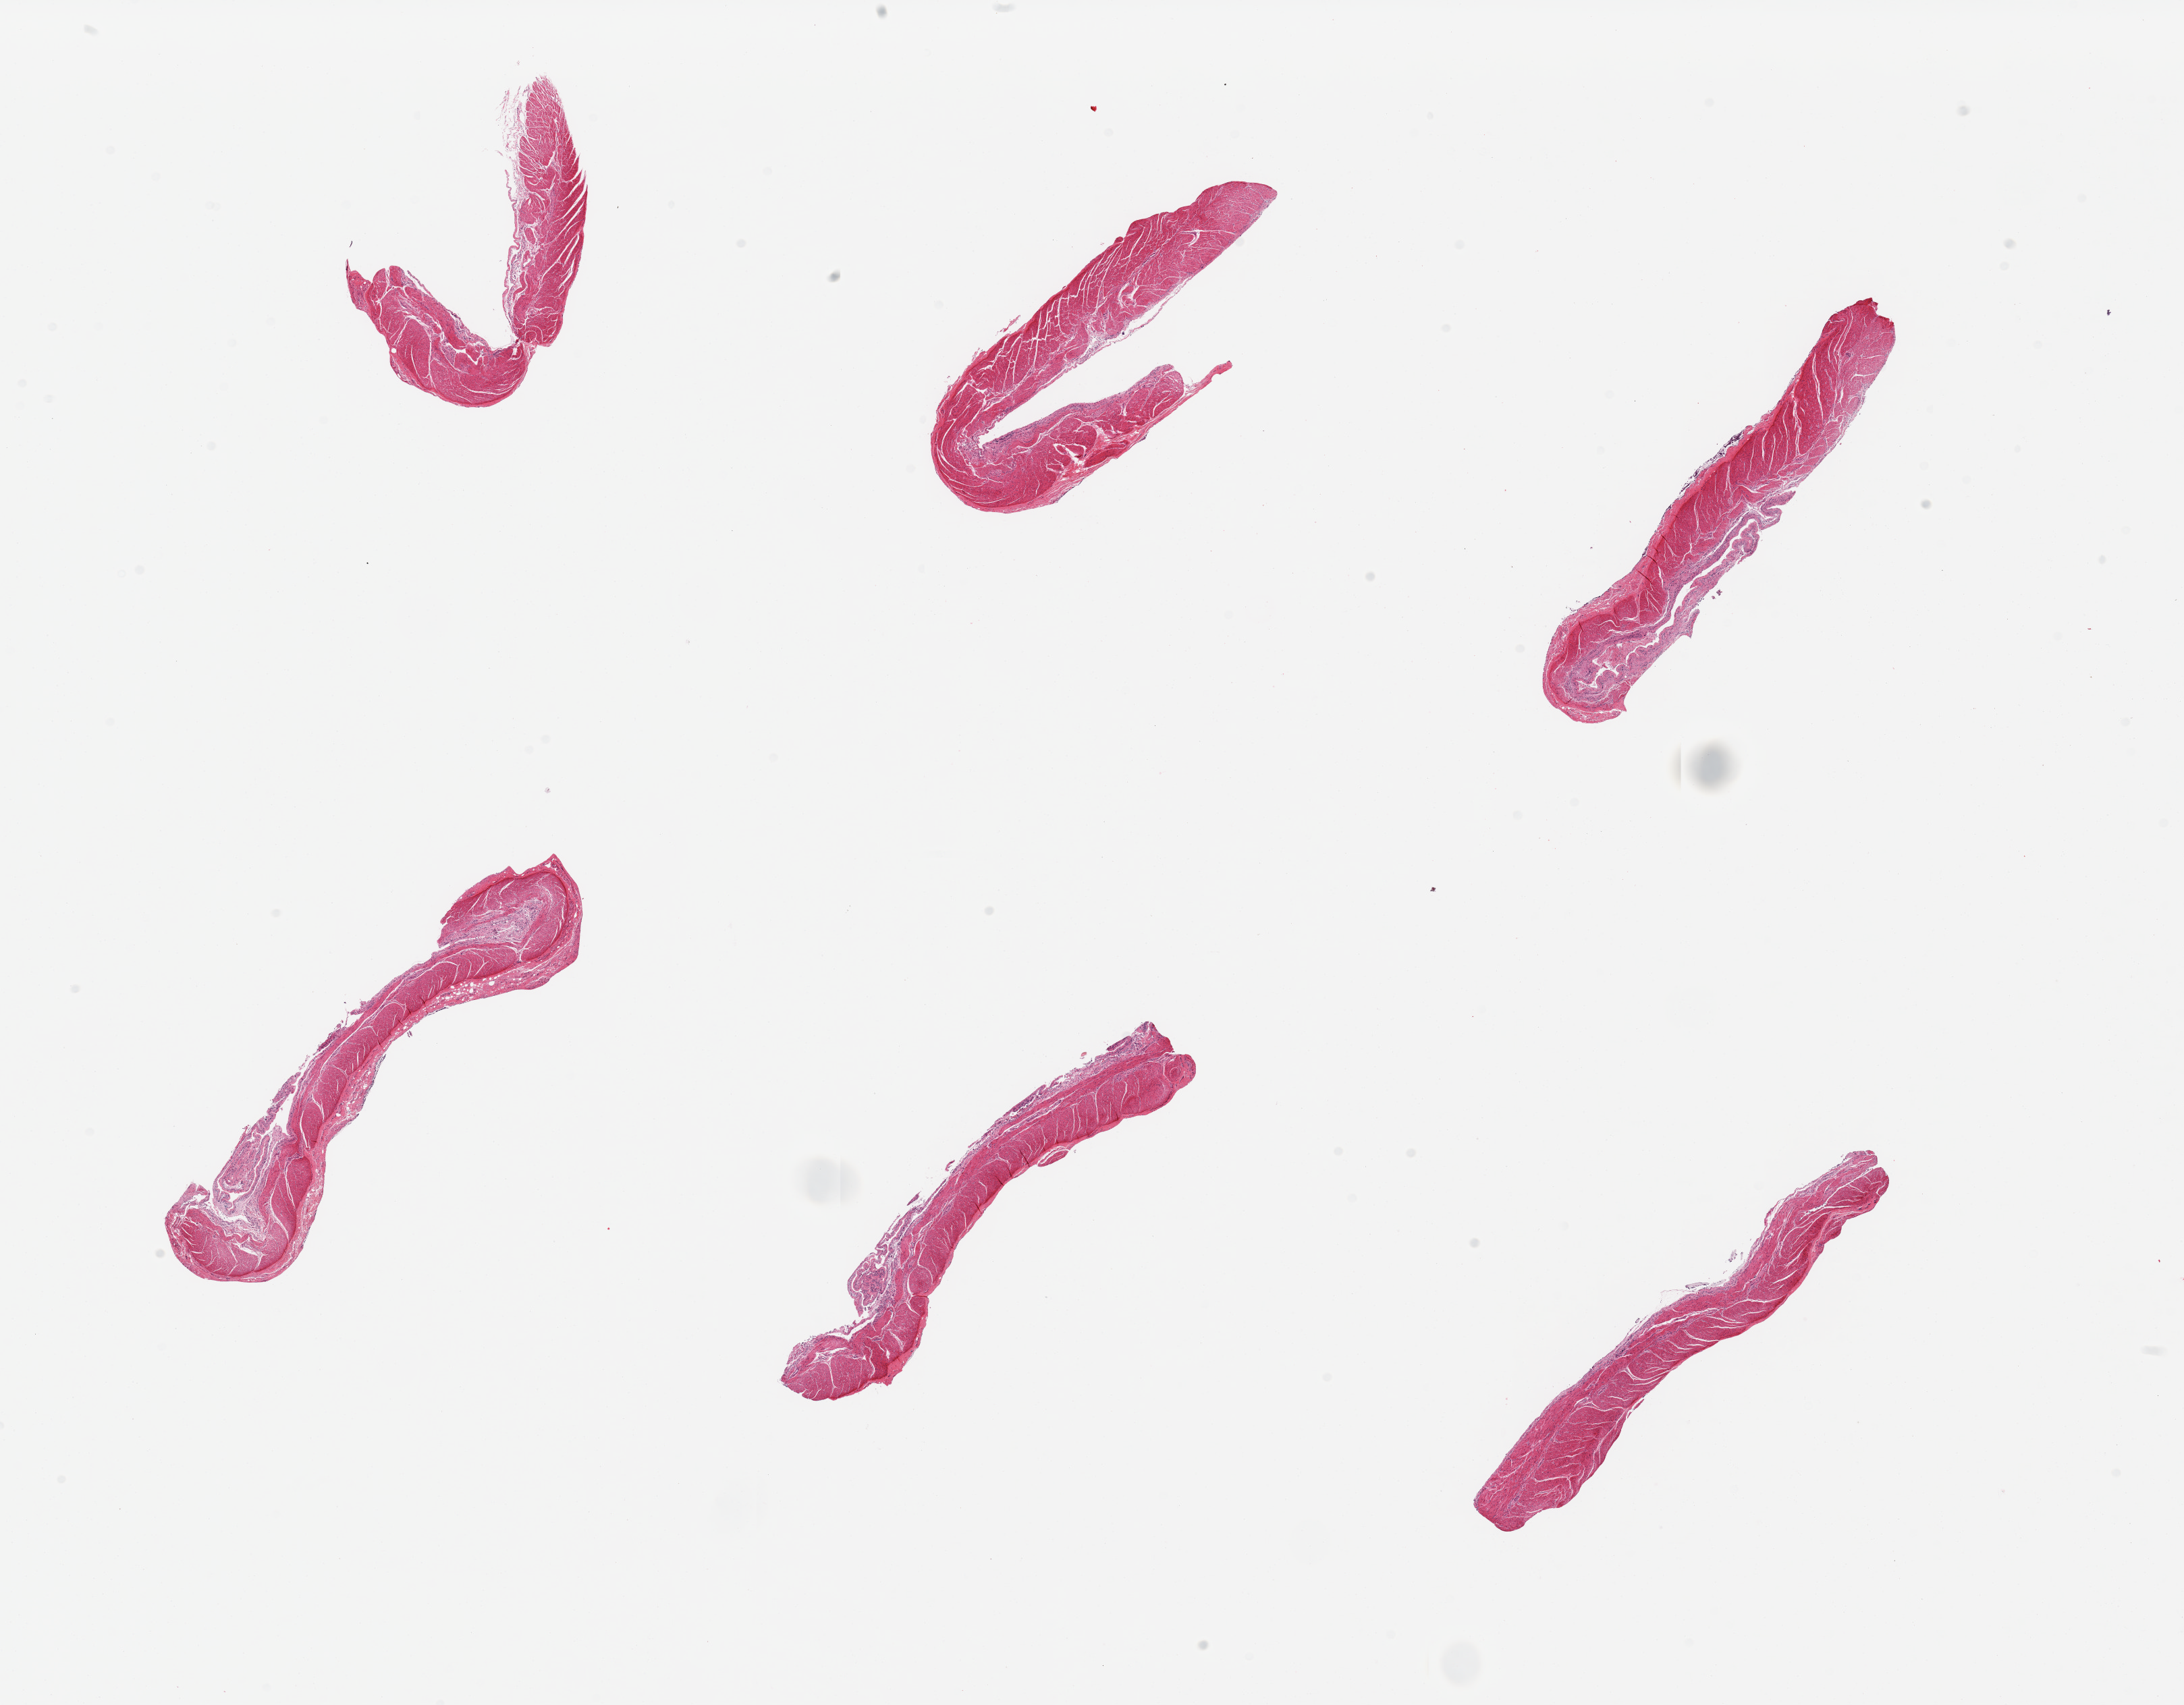
Digitized H&E-stained section — shown as a low-resolution overview of the whole scanned area (about 25.6 x 20.0 mm, acquisition: 20x scan). PAXgene-fixed, paraffin-embedded tissue. Section of sigmoid colon (target tissue). Donor tissue sample. Donor sex: male.
Reviewer comment on this tissue sample: 6 pieces; some residual submucosa/serosa.